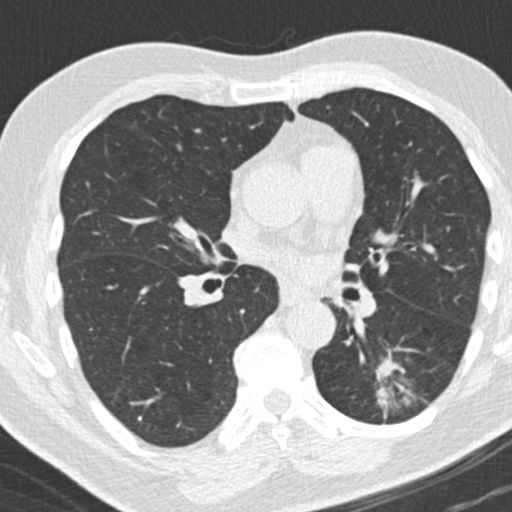
Low-dose screening chest CT, one axial slice. Position 101 of 180 along the scan axis. Reconstruction kernel B30f. Lung window (W 1500 / L -600 HU). 2 mm slice thickness. 512 × 512 image matrix, field of view 300 × 300 mm.
Annotated regions visible in this slice (manually delineated by an expert):
- lesion 1 (tumor, lower lobe of left lung): box from (x=376, y=358) to (x=399, y=378) px